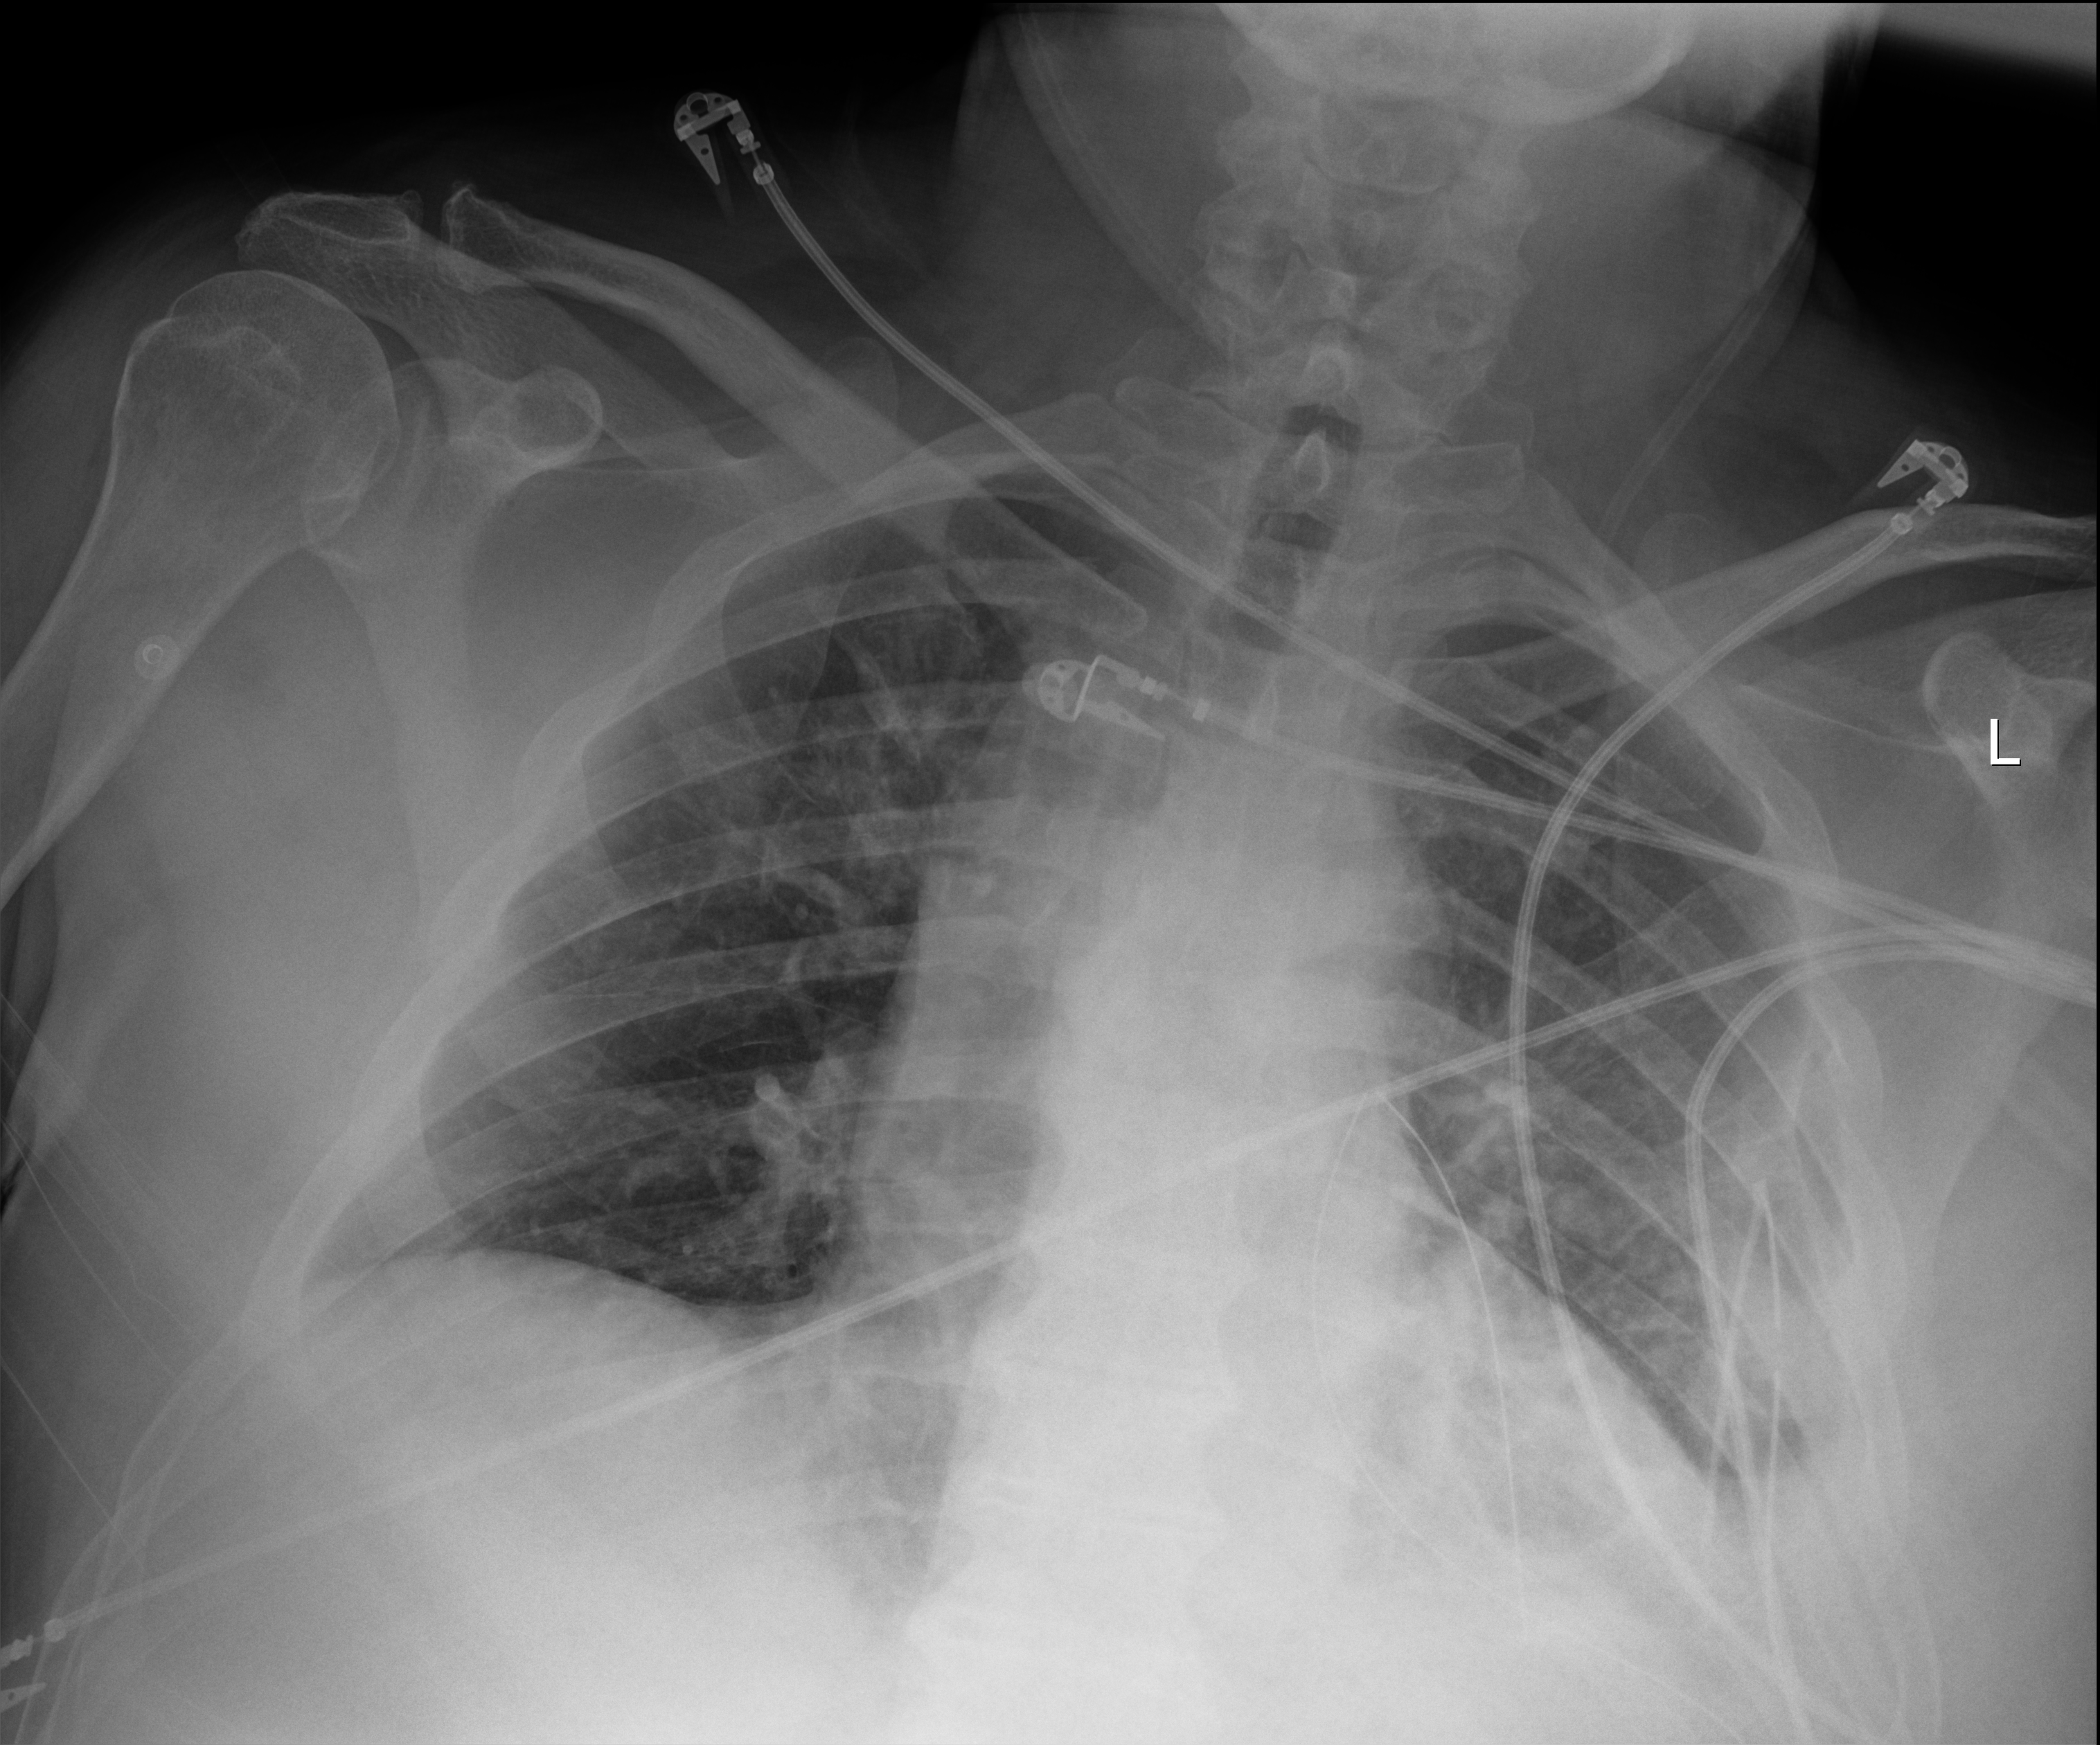
Chest X-ray (portable); anteroposterior (AP) projection. Male patient hospitalised with COVID-19, age 18–59 years.
Hospital-stay facts (about this admission, not read from this image; timing relative to this image not recorded):
- mechanically ventilated during this hospital stay: no
- admitted to intensive care during this hospital stay: no
- length of hospital stay: 10 days